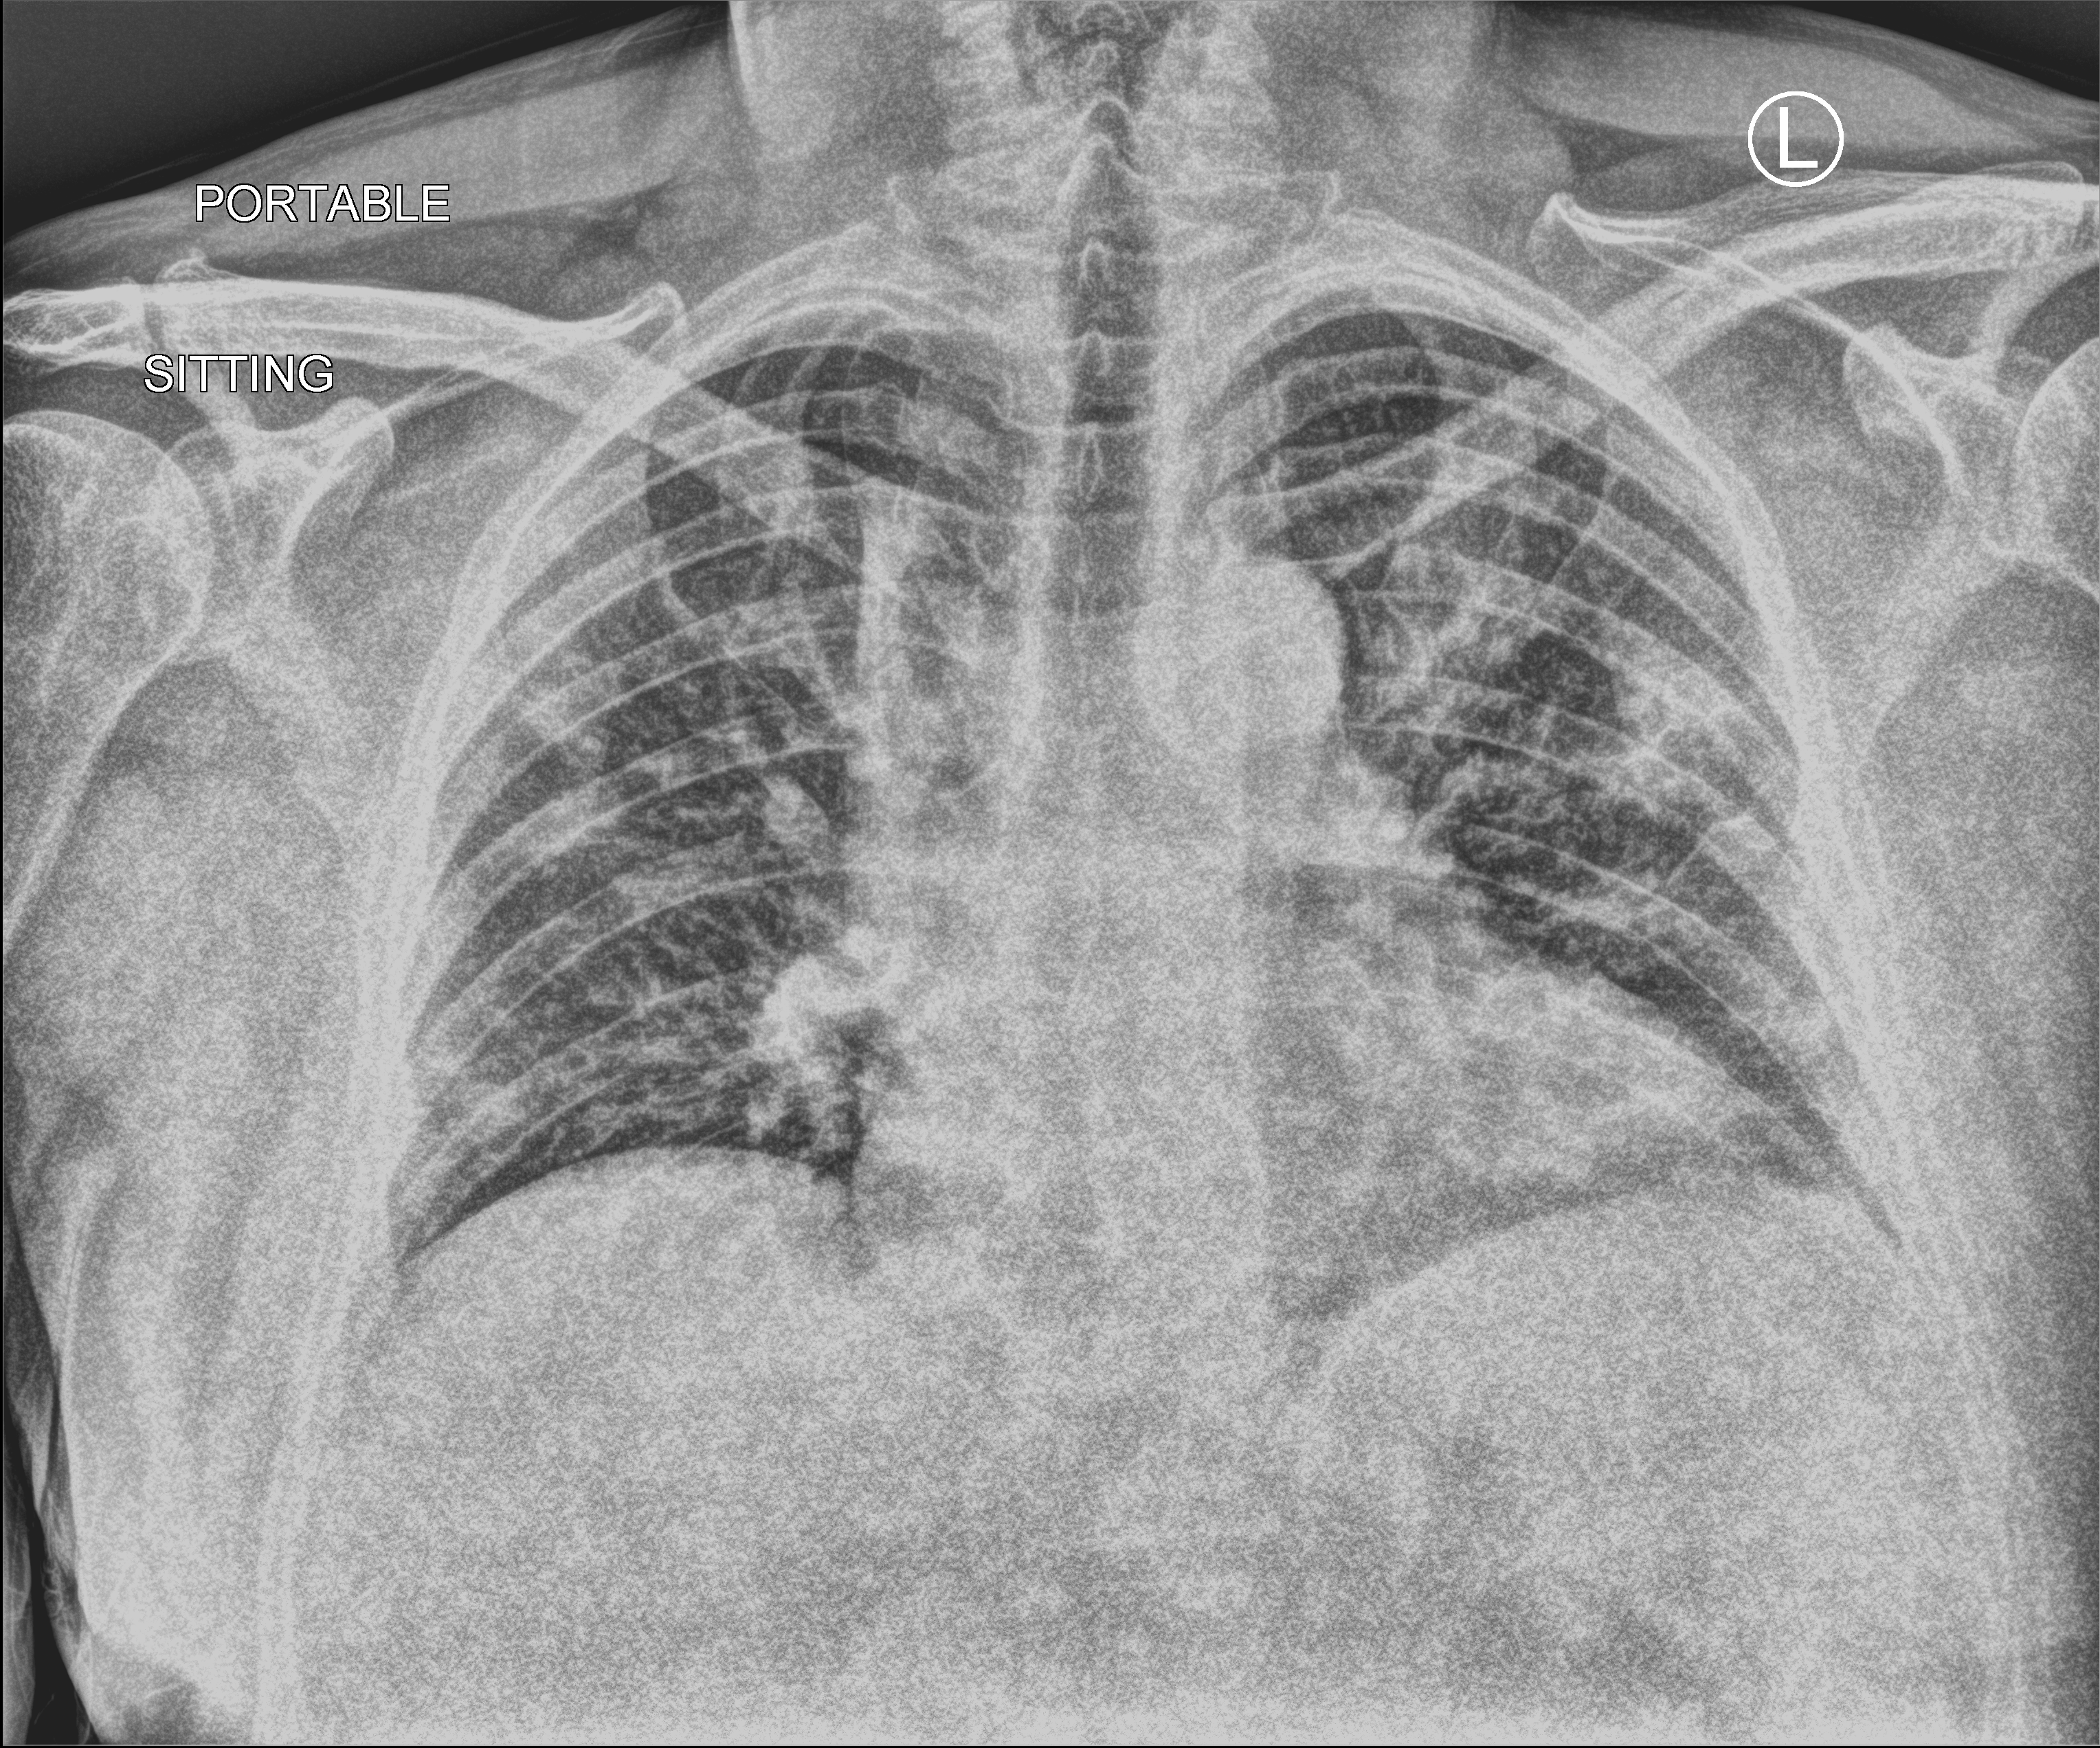
Bedside chest radiograph (computed radiography). Patient hospitalised with COVID-19; male, aged 60–74 years.
Admission-level facts for this patient (not findings on this image; timing relative to this image not recorded): hypertension (admission record): no; diabetes (admission record): no.